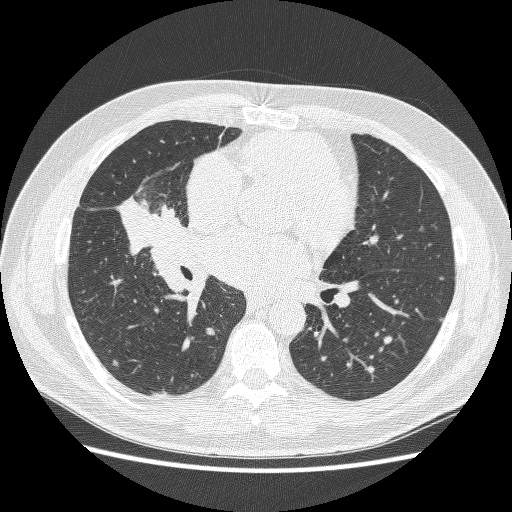
Axial slice from a low-dose chest CT screening exam, baseline screening round, lung window (W 1500 / L -600 HU), 1.25 mm slice thickness, 512 × 512 image matrix. Male, age 59 years at enrolment.
Expert reader's lesion annotation, box from (x=118, y=180) to (x=196, y=257) px. No non-calcified nodule or mass ≥4 mm was recorded by the screening reader at this exam. Later outcome: lung cancer diagnosed 24 days after this screen — adenocarcinoma, NOS, right middle lobe, poorly differentiated (G3), stage IV (AJCC 6th edition), 54 mm at pathology.